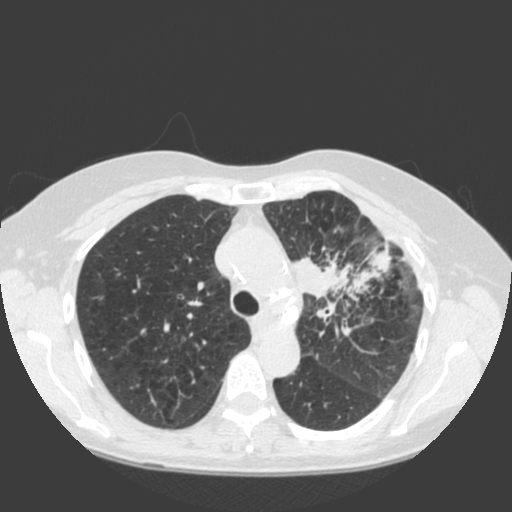
Low-dose screening chest CT, one axial slice. Slice 136 of 184 in the series (ordered by position). 120 kVp. Lung window (W 1500 / L -600 HU). 2 mm slice thickness. 512 × 512 image matrix.
Outlined on this slice (expert manual segmentation):
- lesion 1 (tumor, hilum of left lung): bounding box <293,241,392,320> (left, top, right, bottom; pixels)